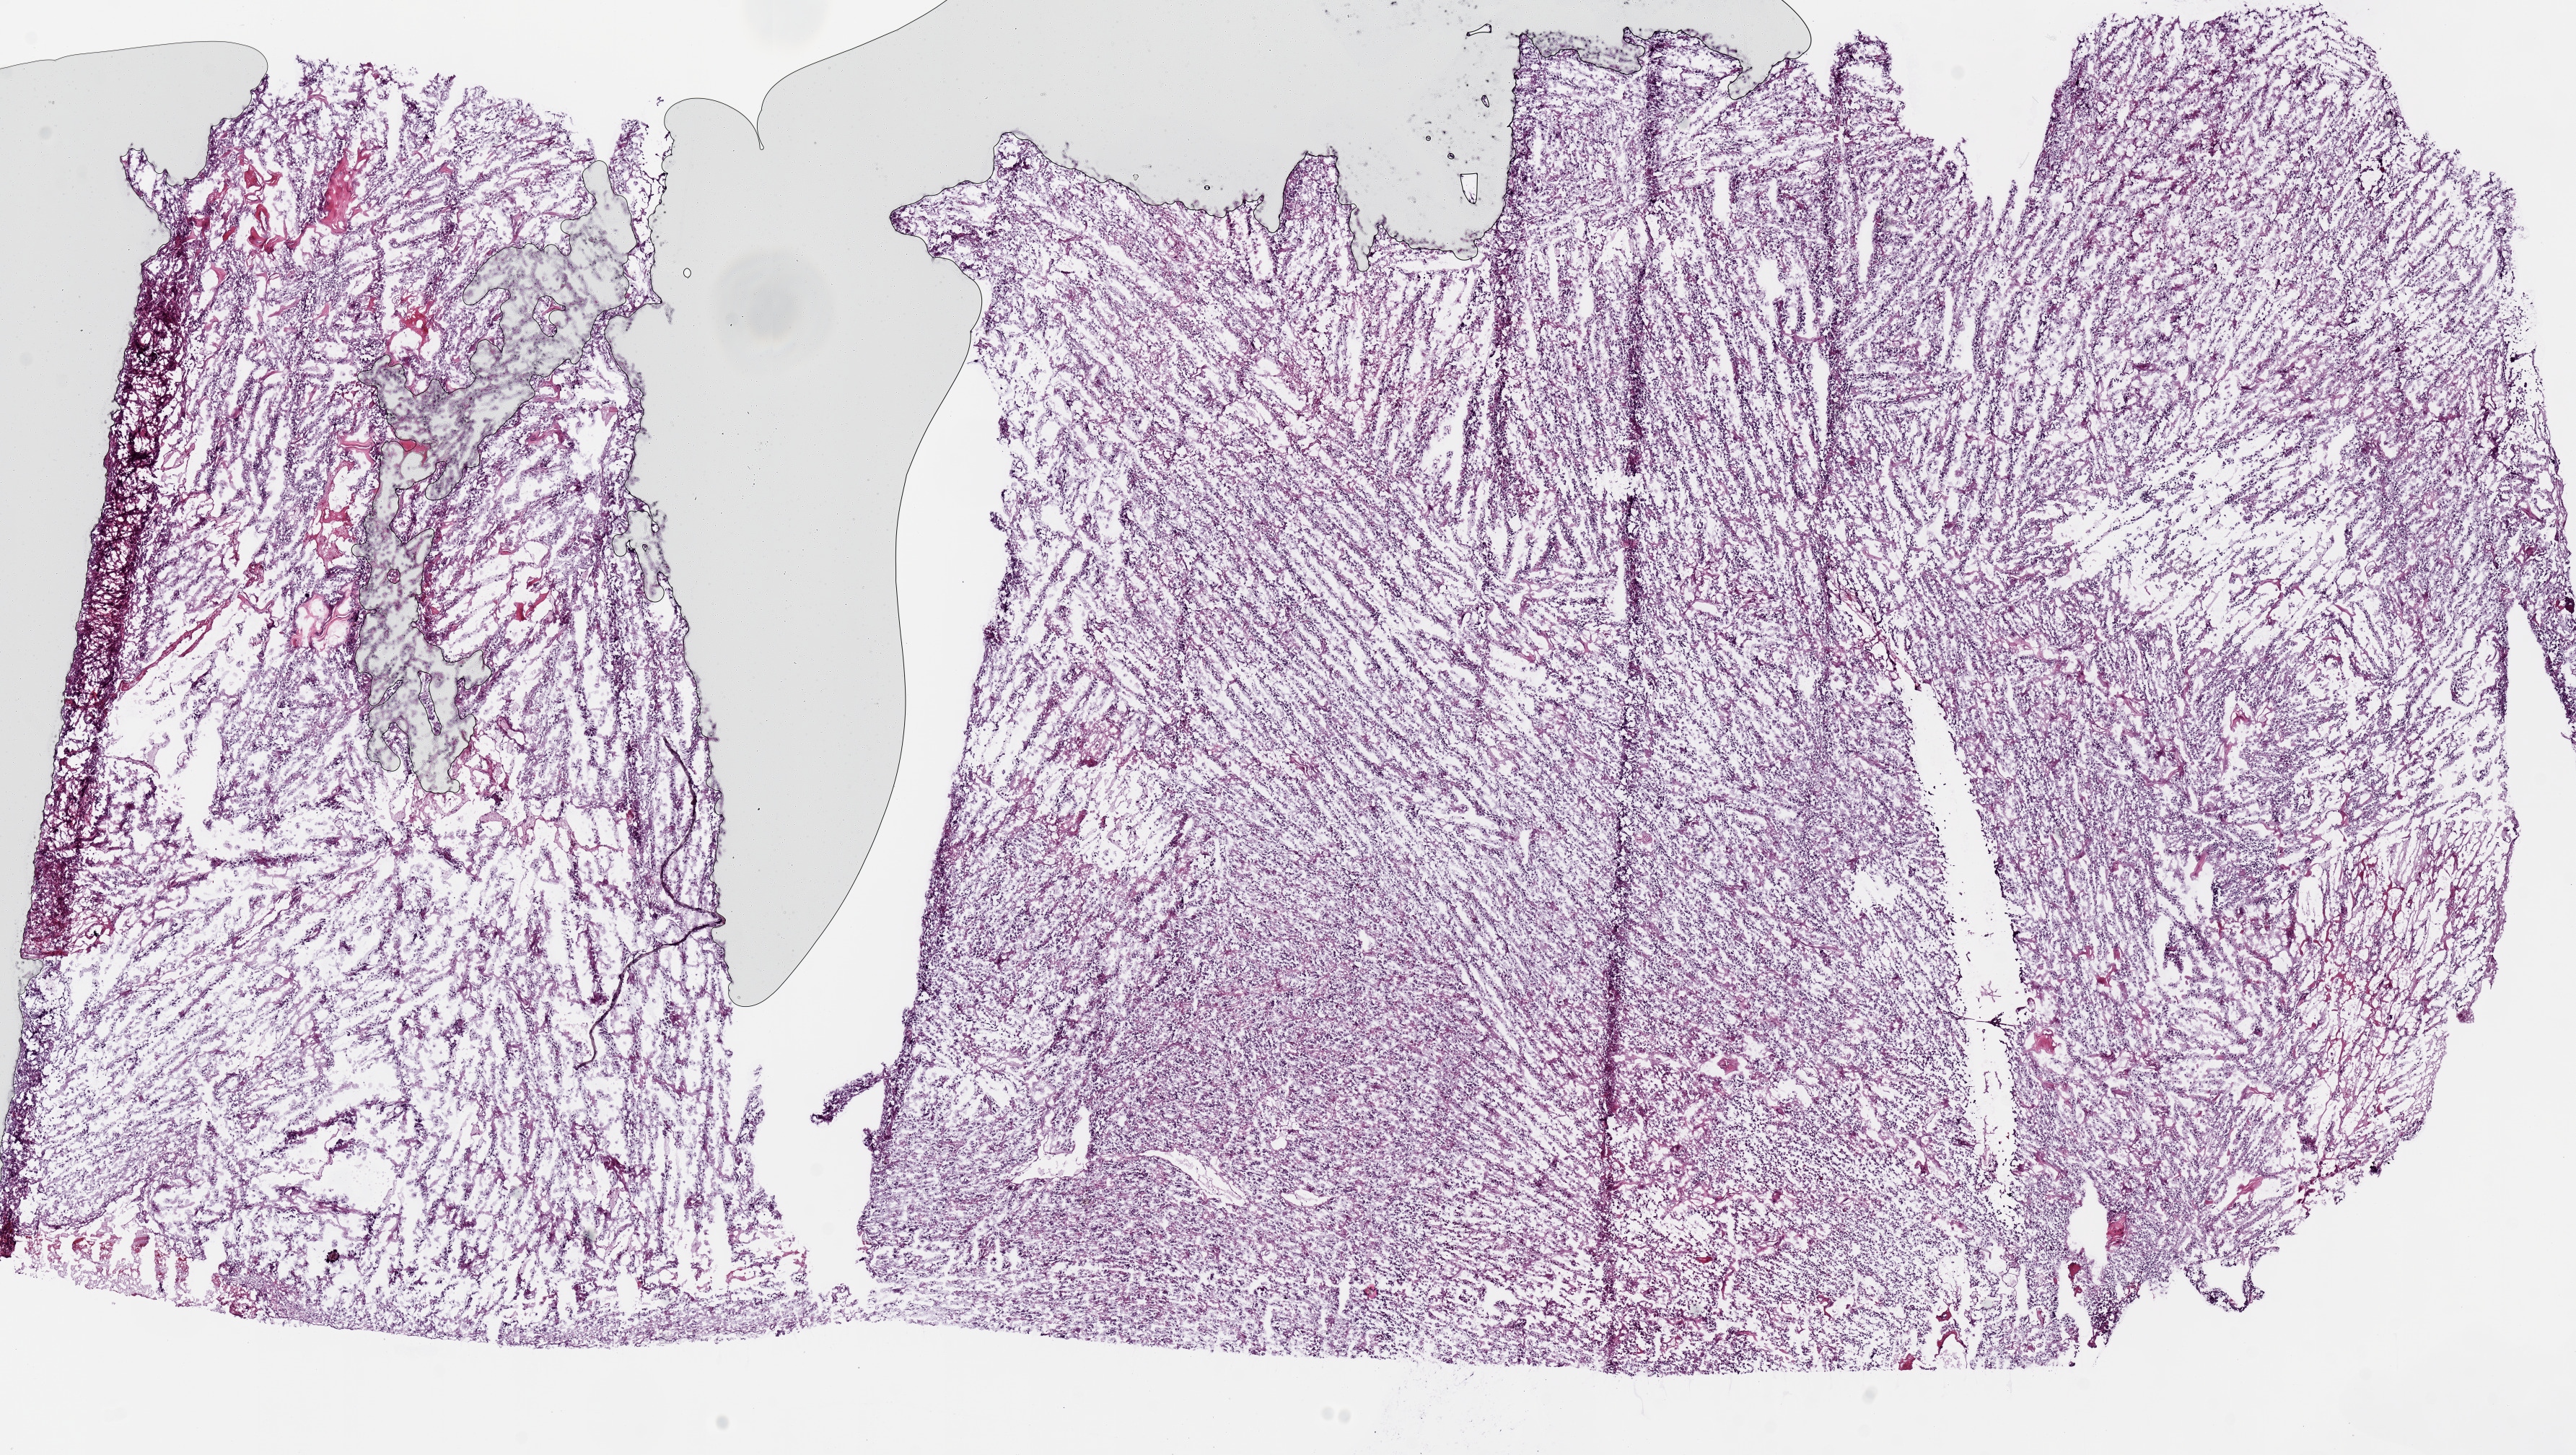
Whole-slide histology image, H&E — shown as a low-resolution overview of the whole scanned area (about 14.2 x 8.0 mm), frozen section, brain, primary tumour sample. Female patient; age at initial diagnosis 53 years. Histologic grade: G3 (poorly differentiated). Pathologist review of this section (percent, as recorded): tumour cells 100%, tumour nuclei 85%, normal cells 0%, stromal cells 0%, necrosis 0%.
- pathologic diagnosis: Oligodendroglioma, anaplastic
- laterality: right